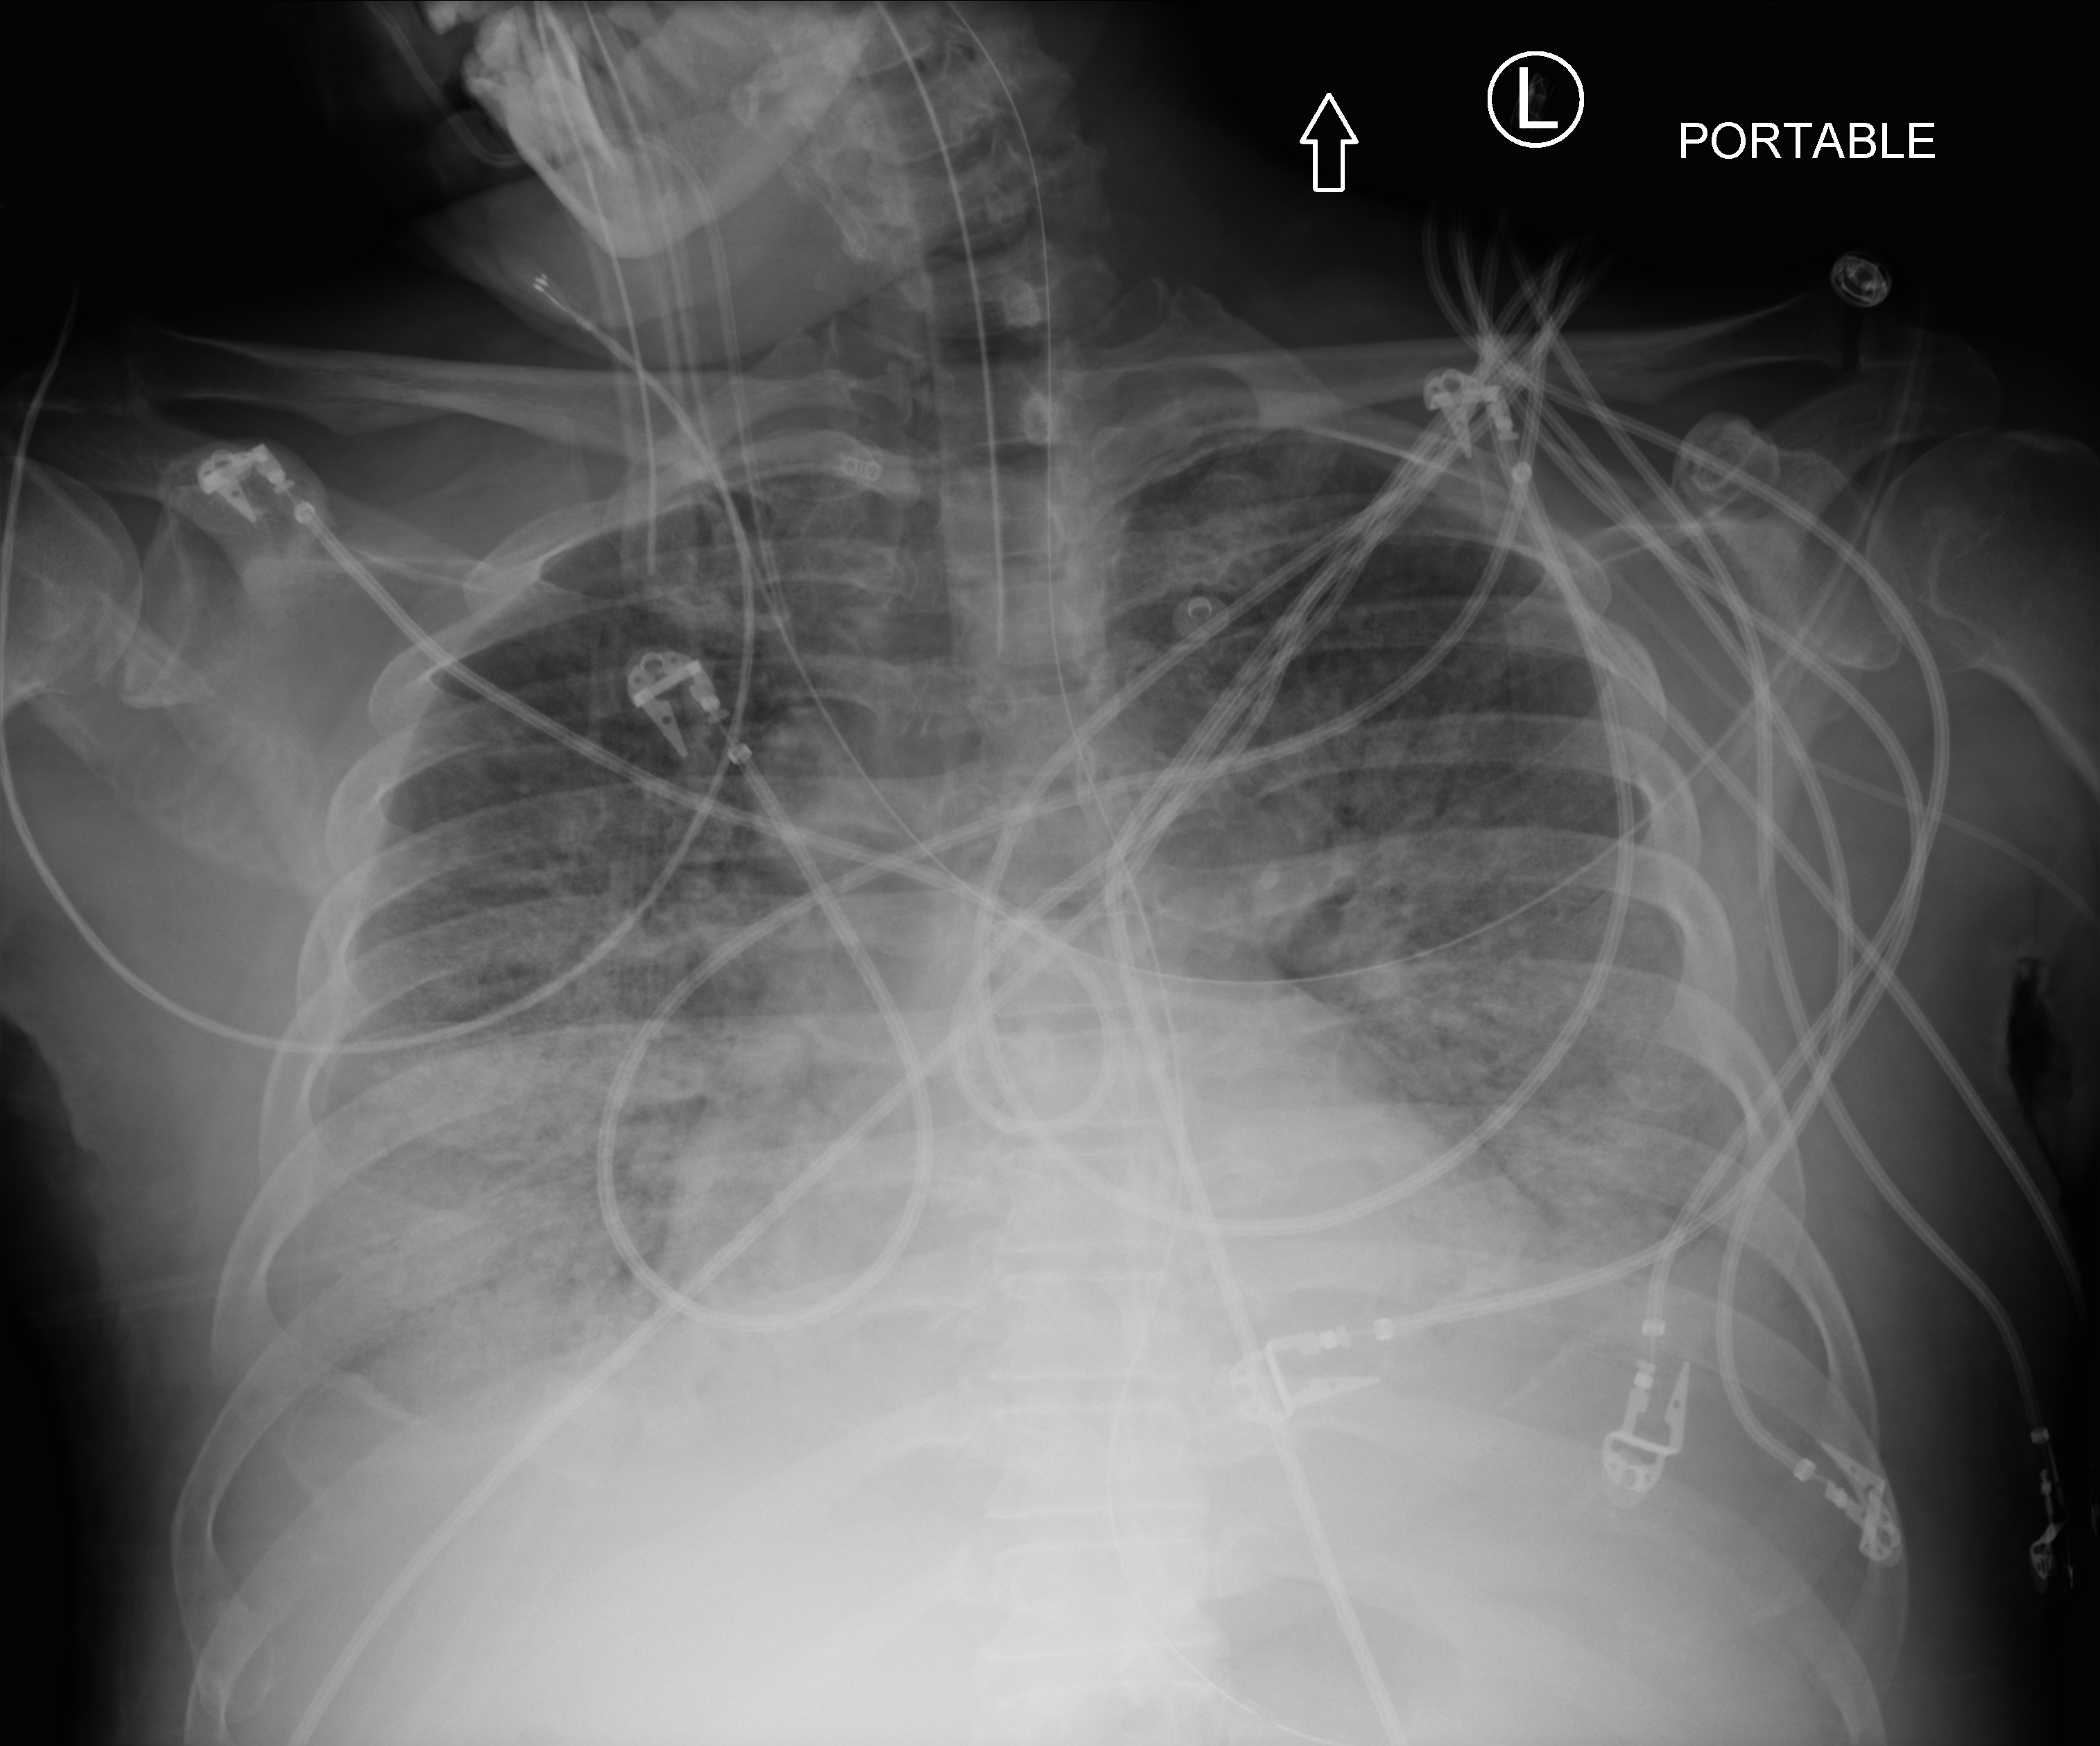
Chest X-ray (portable); anteroposterior (AP) projection. Male patient hospitalised with COVID-19, age 60–74 years.
Admission-level facts for this patient (not findings on this image; timing relative to this image not recorded): COPD (admission record): no.